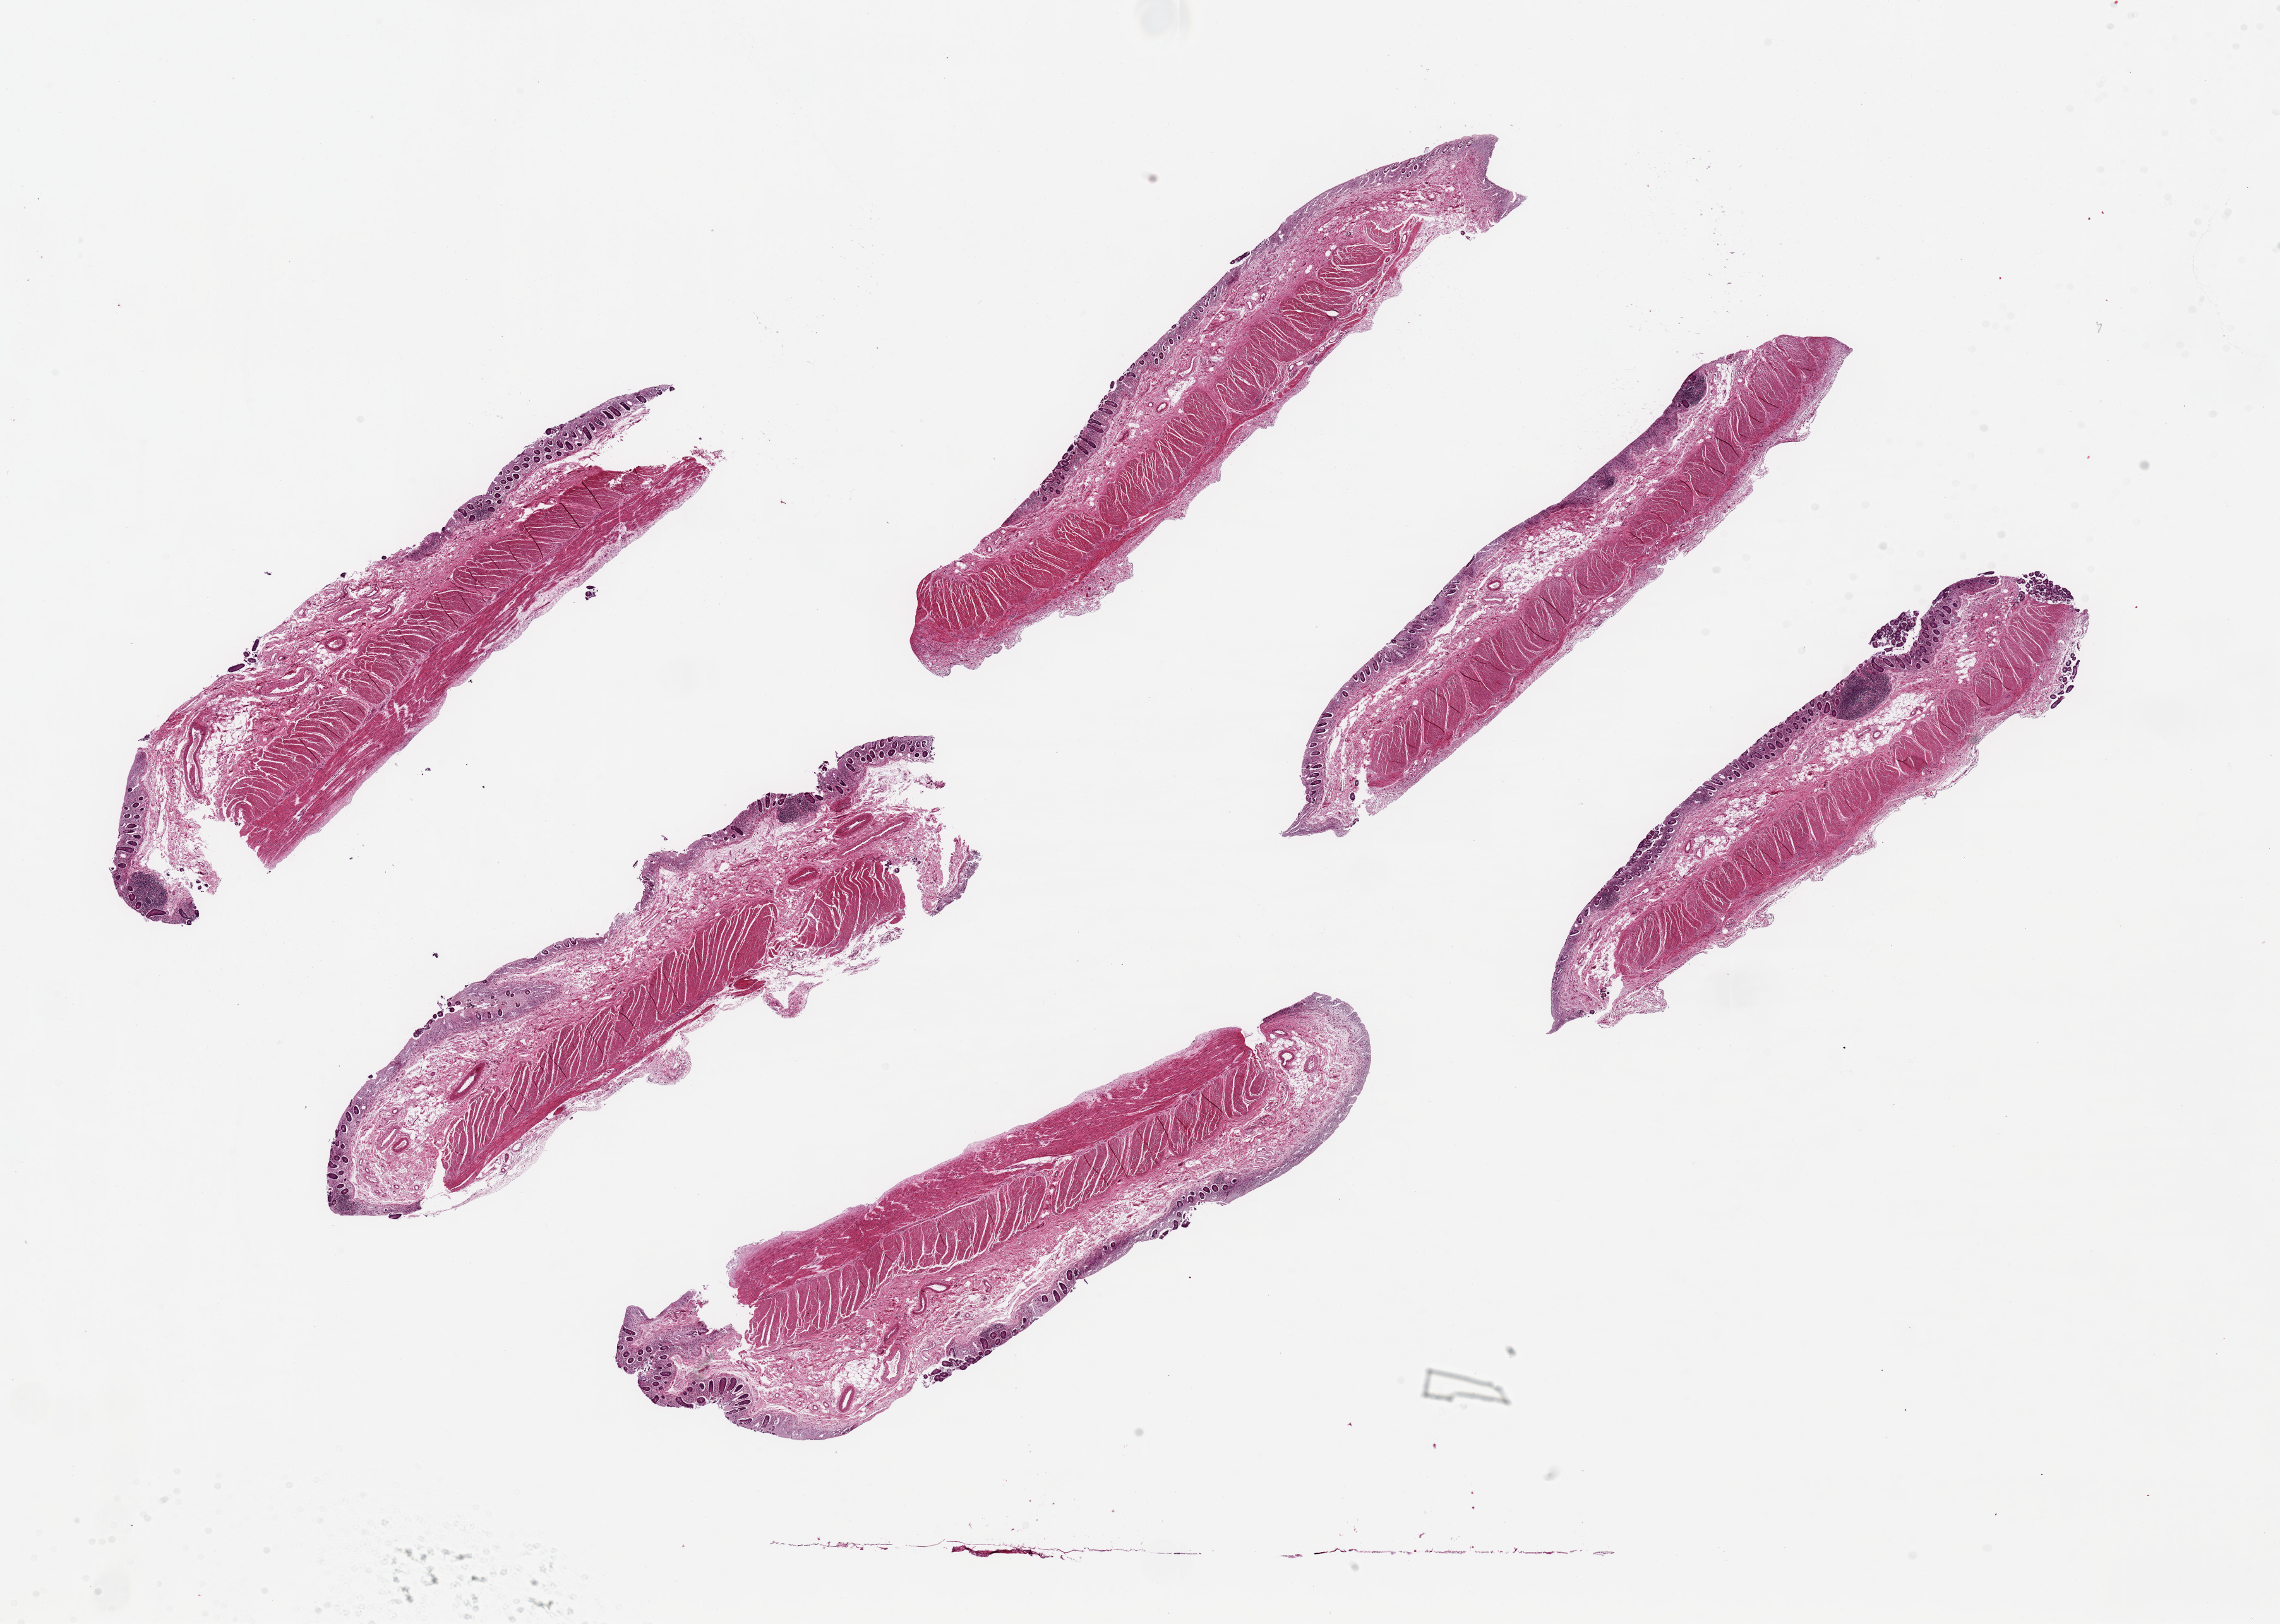
Whole-slide image, H&E stain — a low-resolution overview of the entire scanned area, about 28.5 x 20.3 mm (from a 20x scan). PAXgene-fixed paraffin-embedded (PFPE) section. Target tissue: transverse colon. Tissue donor sample. Donor sex: male.
• reviewer comment on this tissue sample: 6 pieces, ~10x2.5mm, poorly preserved mucosa